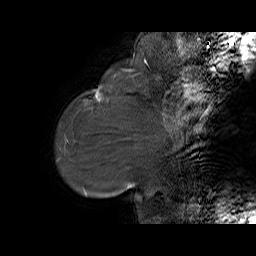
Breast MRI (dynamic contrast-enhanced), one sagittal slice. Slice 11 of 65 in the series (ordered by position). Dynamic contrast-enhanced series, time point 2 of 6 at this slice position (early post-contrast). 1.5 T. TE 5.7 ms, TR 32.9 ms. 4 mm slice thickness. 256 × 256 image matrix, field of view 230 × 230 mm. Female patient. From the clinical record (not read from this slice): setting: breast cancer imaged before/during neoadjuvant chemotherapy; receptor status: HER2-positive.
Outlined on this slice (semi-automatic segmentation, software-assisted and operator-edited):
- analysis volume of interest (the breast-tissue region the enhancement analysis was run in; not a lesion): bounding box [x1, y1, x2, y2] px = [85, 77, 125, 111]
- tumour enhancement mask (voxels above the 100 % enhancement threshold inside the analysis volume of interest): [95, 91, 101, 100]